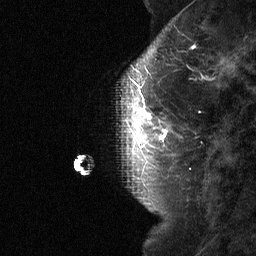
Breast MRI (dynamic contrast-enhanced), one sagittal slice. Position 16 of 64 along the scan axis. Dynamic contrast-enhanced study with each time point stored as its own series, time point 2 of 3 at this slice position (early post-contrast, ordered by acquisition time). 1.5 T. TE 4.8 ms, TR 27 ms. 2 mm slice thickness. 256 × 256 image matrix, field of view 180 × 180 mm. Patient: female, 42 years. Case-level facts recorded for this patient, not image findings: setting: breast cancer imaged before/during neoadjuvant chemotherapy; receptor status: triple-negative.
Annotated regions visible in this slice (semi-automatic segmentation, software-assisted and operator-edited):
- analysis volume of interest (the breast-tissue region the enhancement analysis was run in; not a lesion): bounding box (x1, y1, x2, y2) in pixels: (116, 85, 175, 160)
- tumour enhancement mask (voxels above the 90 % enhancement threshold inside the analysis volume of interest): (138, 88, 167, 141)